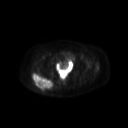
FDG PET of an extremity soft-tissue mass (from a PET/CT study), one axial slice; slice 51 of 267 in the series (ordered by position); 128 × 128 image matrix, field of view 600 × 600 mm. Female patient, age 60 years. Case-level facts recorded for this patient, not image findings: histological type: spindle cell suggestive of myxofibrosarcoma; grade: intermediate; site of the primary tumour: right buttock.
Structures marked on this image (expert contour drawn on MRI and transferred to this co-registered scan by the dataset authors):
- gross tumour volume (mass): bounding box <32,72,53,91> (left, top, right, bottom; pixels)